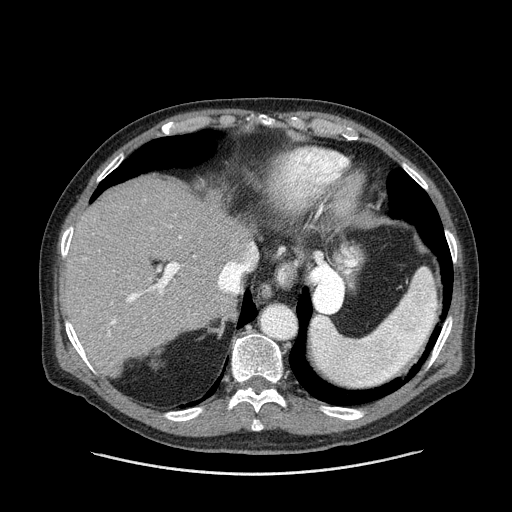
Contrast-enhanced abdominal CT (liver protocol), one axial slice. Position 110 of 180 along the scan axis. Reconstruction kernel STANDARD. 120 kVp. One of 2 acquisitions stored at this slice position. Soft-tissue window (W 400 / L 40 HU). 2.5 mm slice thickness. 512 × 512 image matrix. Case-level facts recorded for this patient, not image findings: diagnosis: hepatocellular carcinoma (patient treated with transarterial chemoembolisation; whether this scan precedes or follows treatment is not stated here); TNM stage (as recorded): Stage-II; Child-Pugh class: A; tumour differentiation: well differentiated.
Outlined on this slice (semi-automatic segmentation, software-assisted and operator-edited):
- liver parenchyma outside the tumour (the mass and vessels are separate outlines, so this box may not span the whole liver): bounding box [x1, y1, x2, y2] px = [64, 176, 256, 374]
- liver vessels: [83, 236, 256, 363]